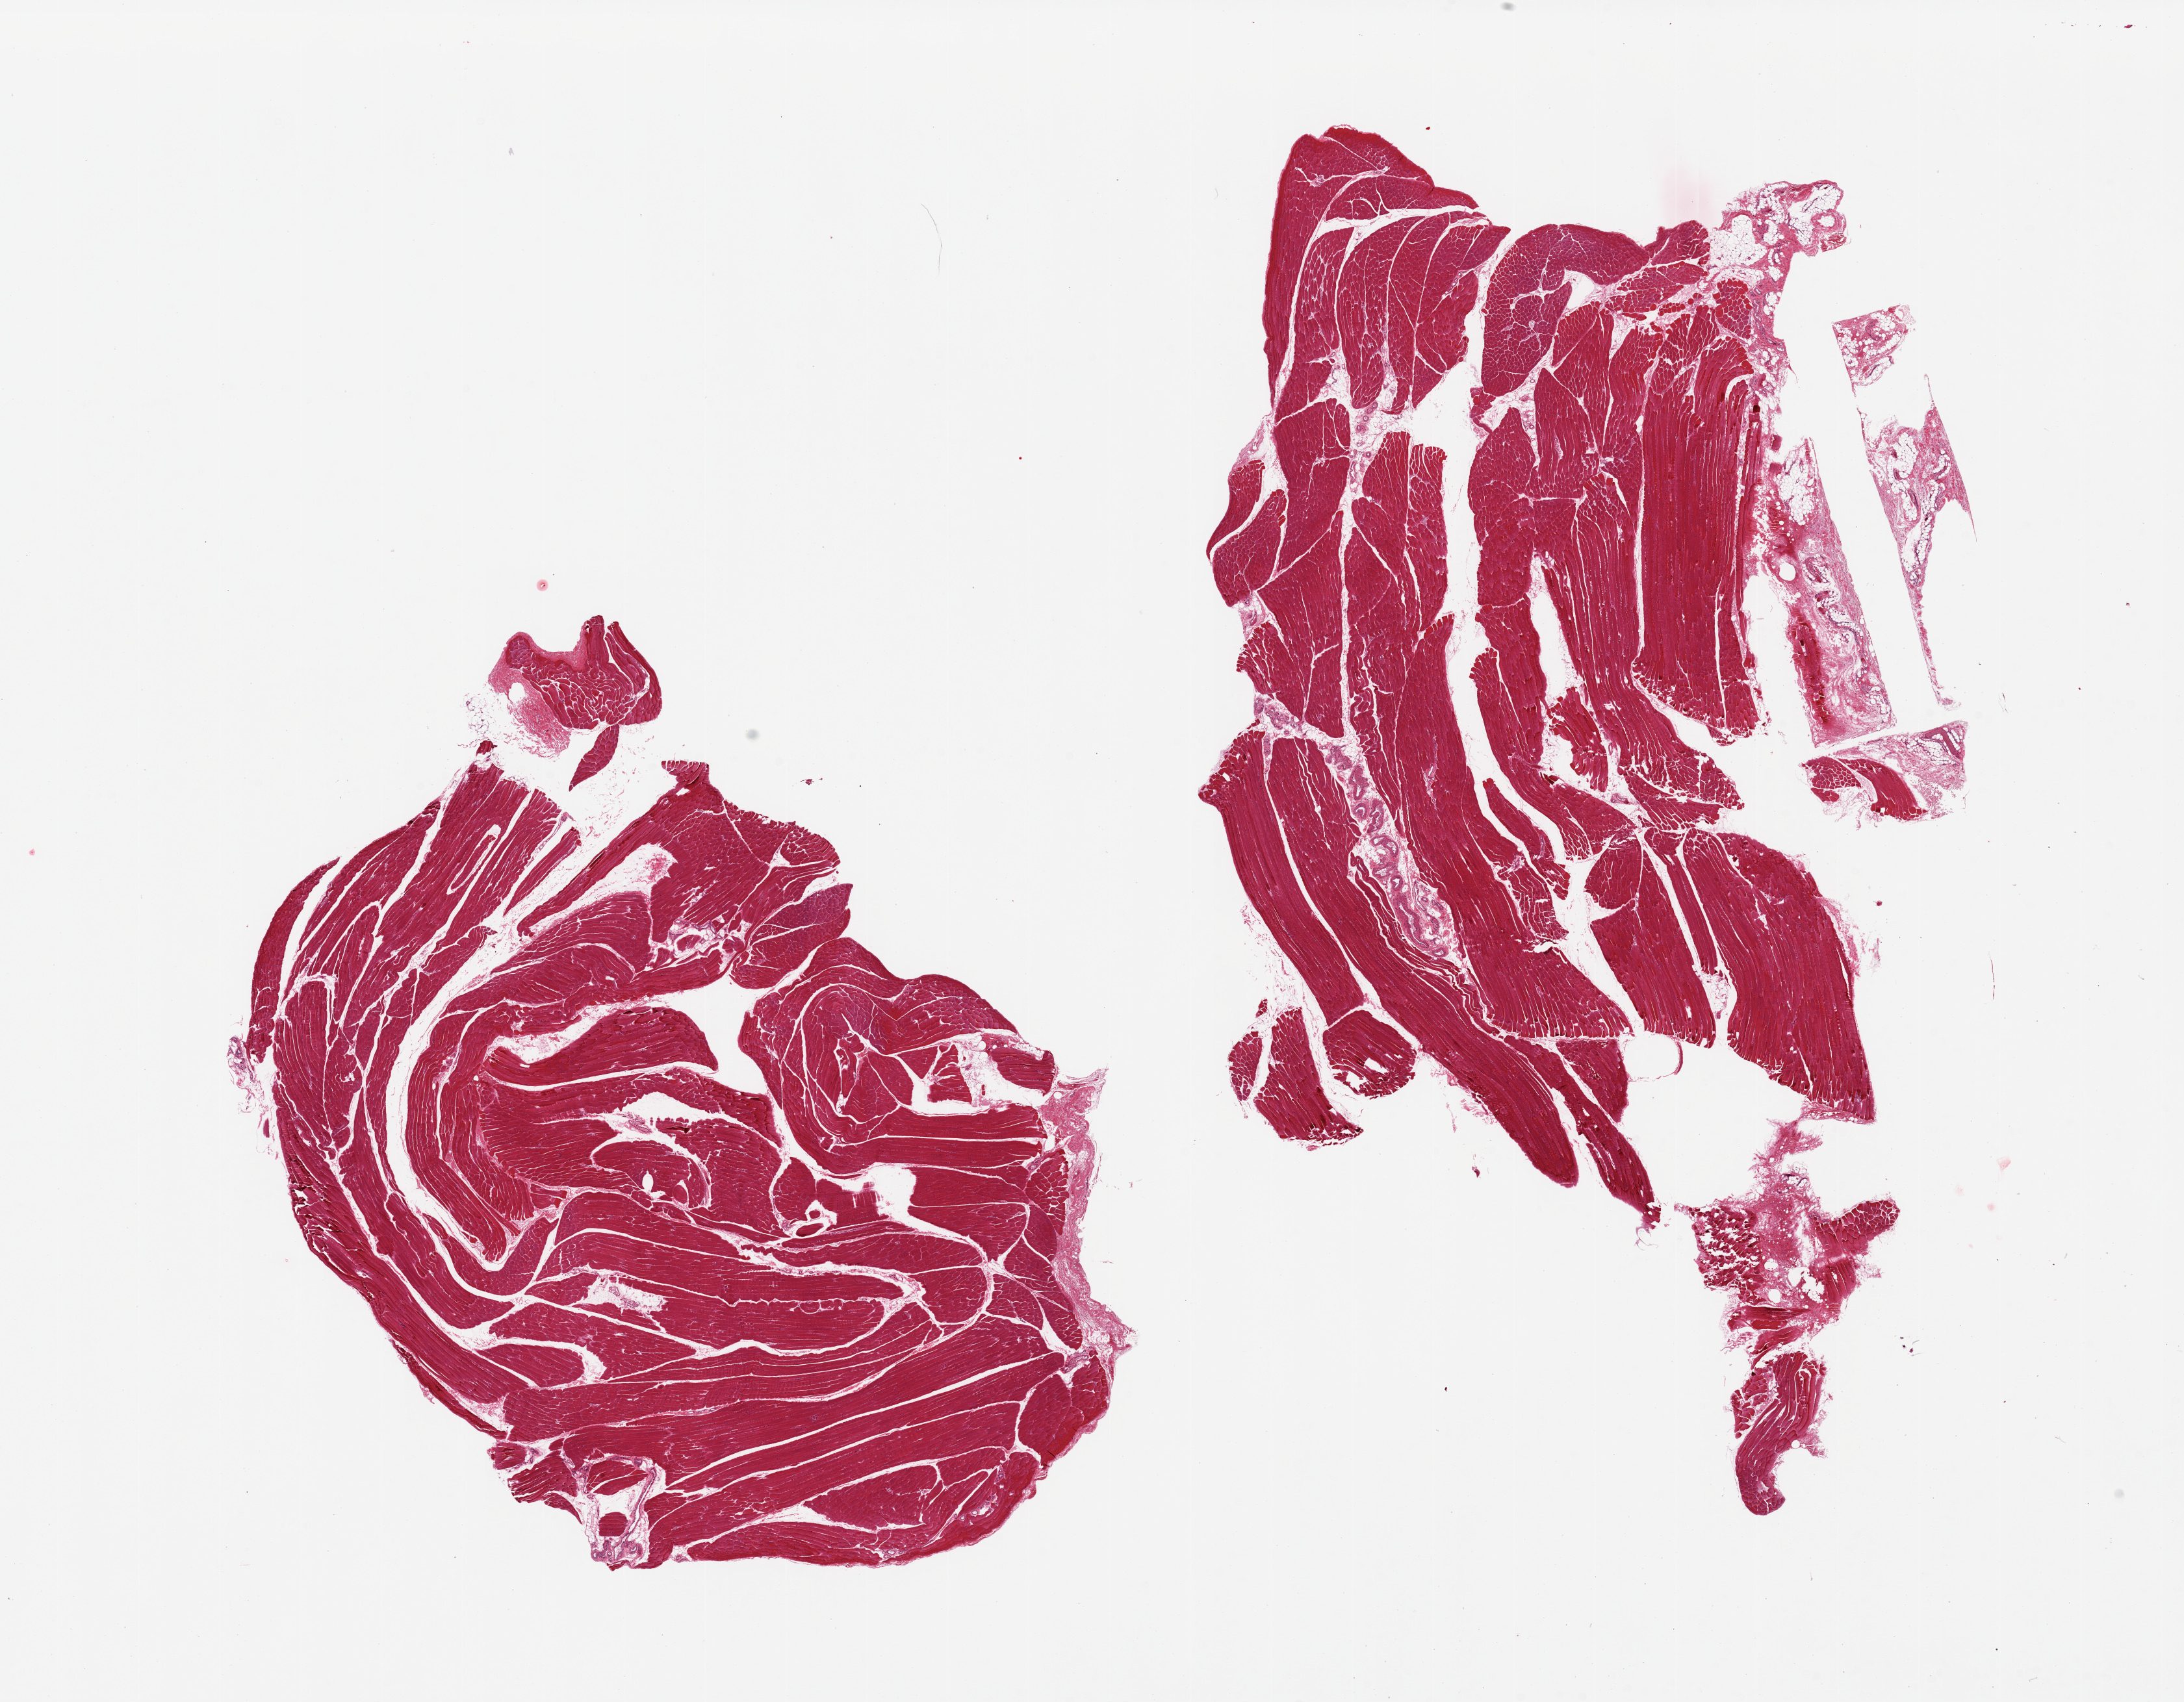
Whole-slide image, haematoxylin and eosin stain, brightfield — low-resolution overview of the scanned area, about 26.6 x 20.7 mm (acquisition: 20x scan). PAXgene-fixed paraffin-embedded (PFPE) section. Sampled site (target tissue): skeletal muscle. Donor tissue sample. Male donor.
Reviewer comment on this tissue sample: 2 pieces.